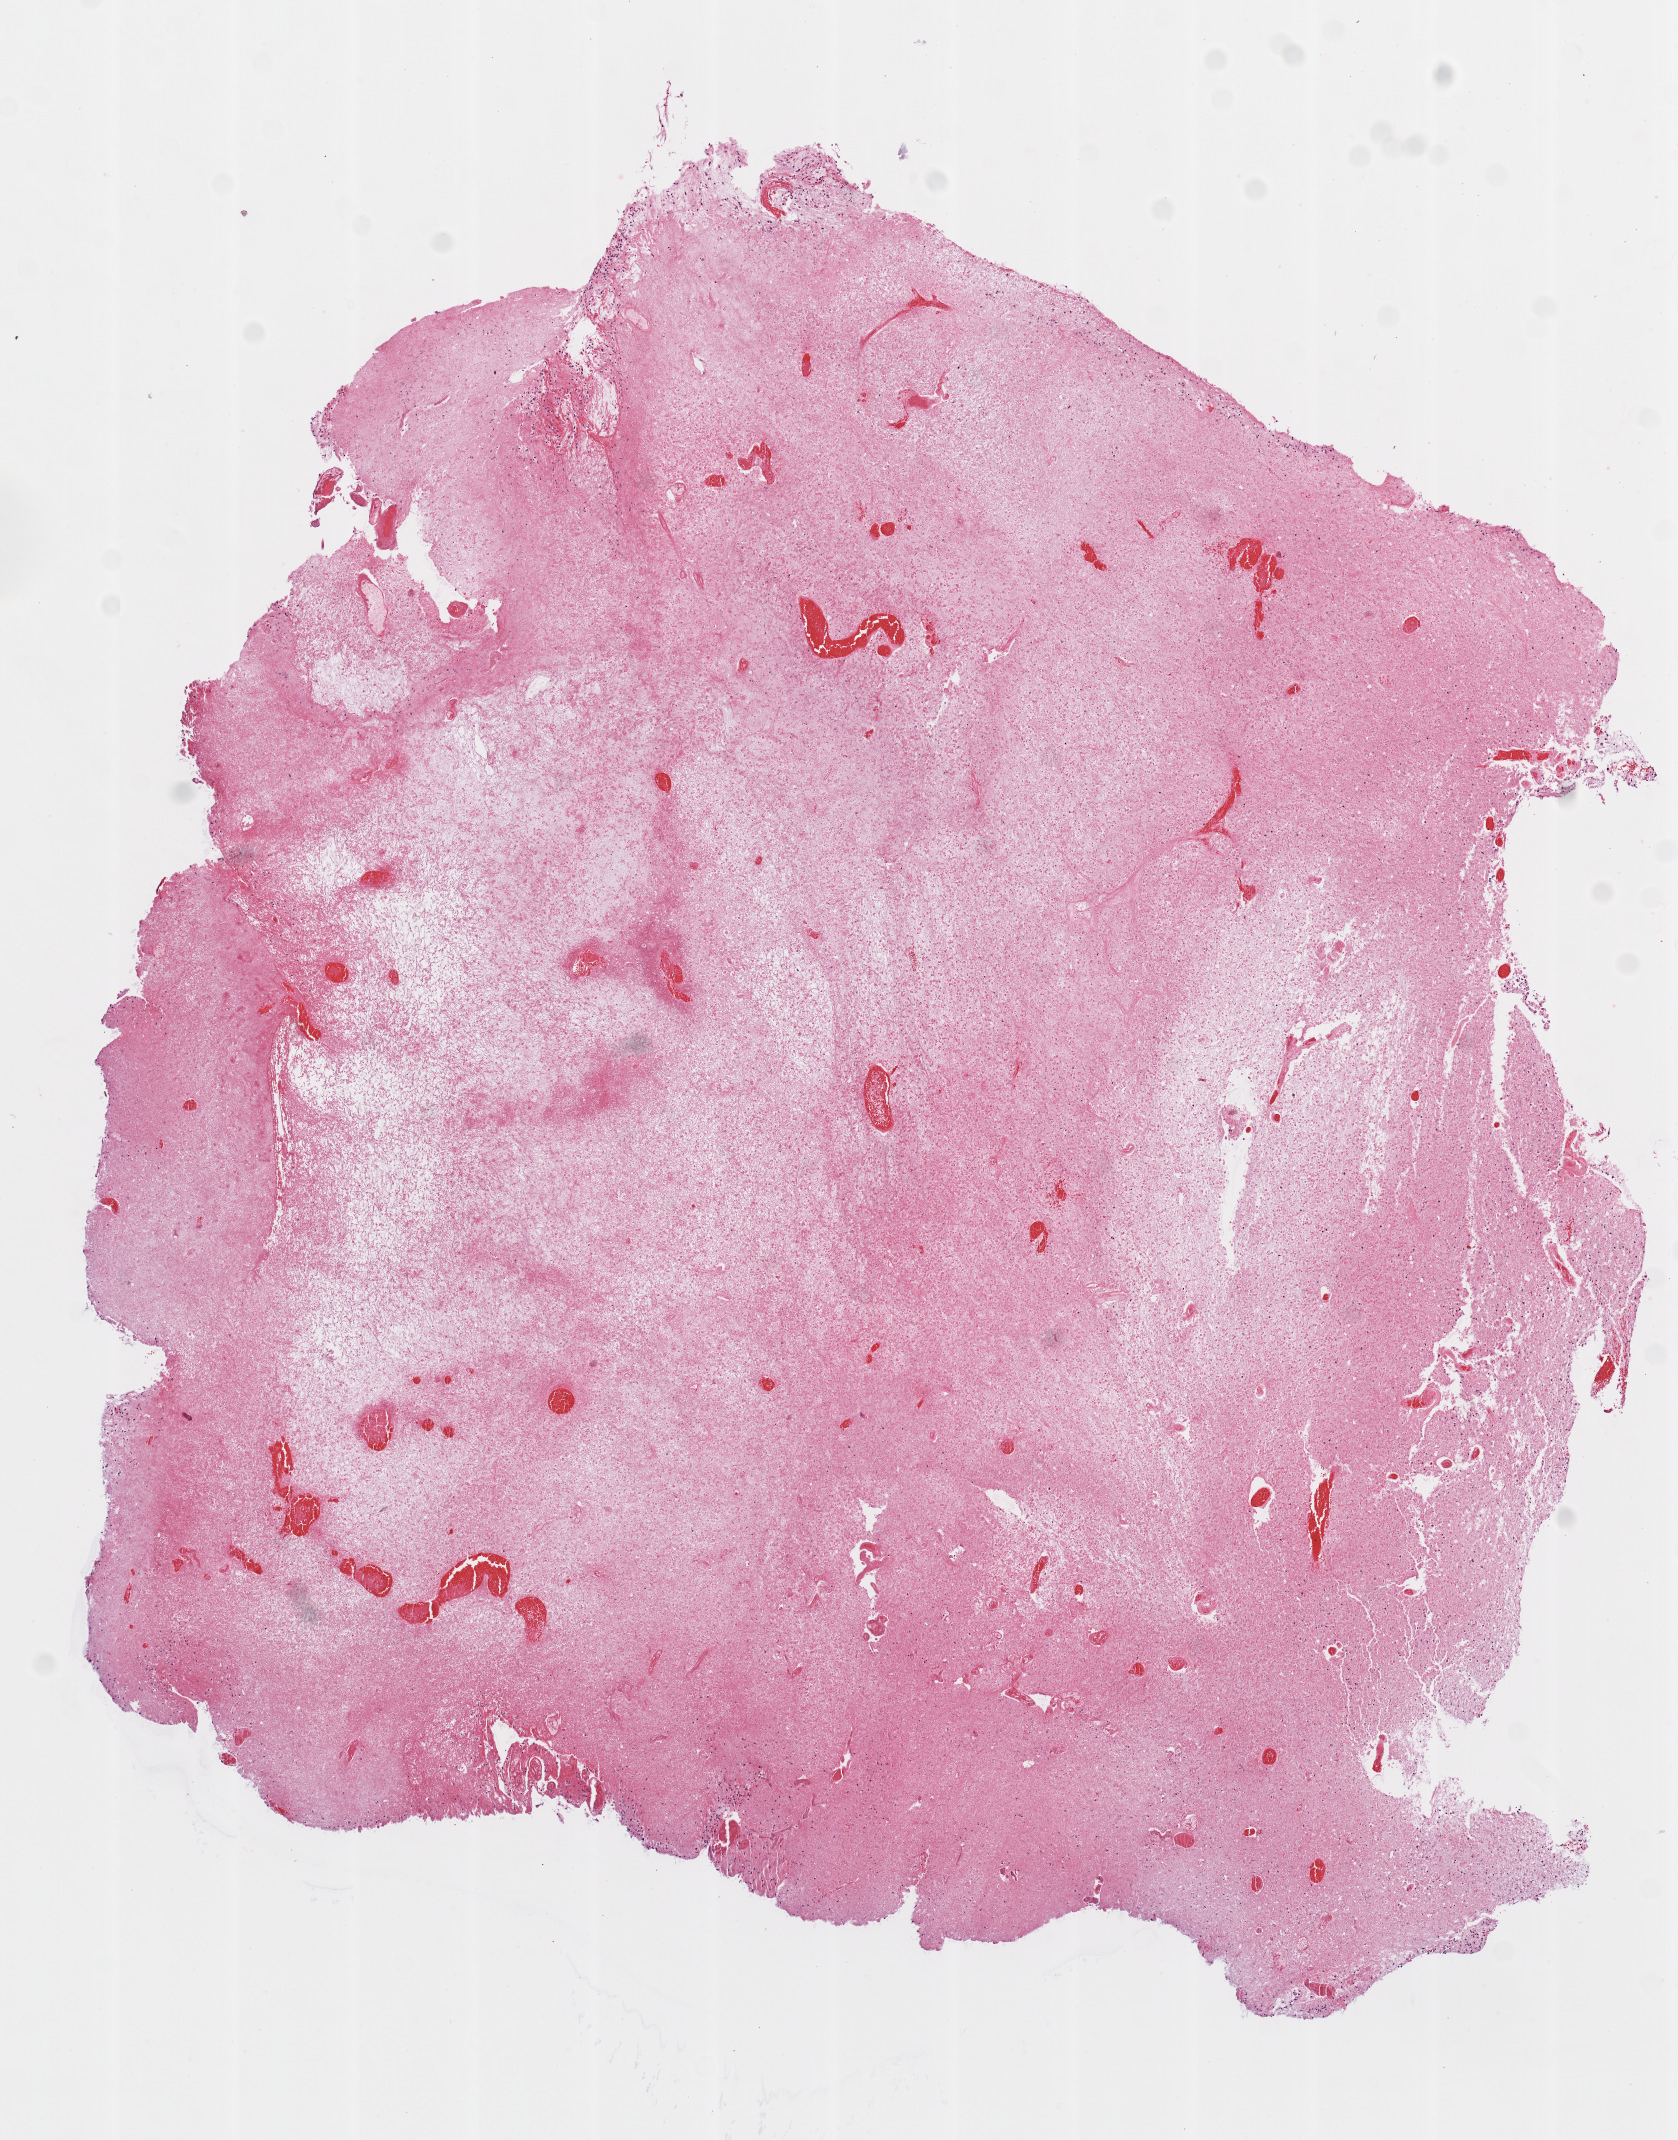
Whole-slide histology image, H&E-stained, a low-resolution overview of the entire scanned area, about 6.8 x 8.6 mm (from a 20x scan), formalin-fixed paraffin-embedded (FFPE) diagnostic section, sample: primary tumour, brain. Male, age 86 years at initial diagnosis.
Diagnosis: Glioblastoma.